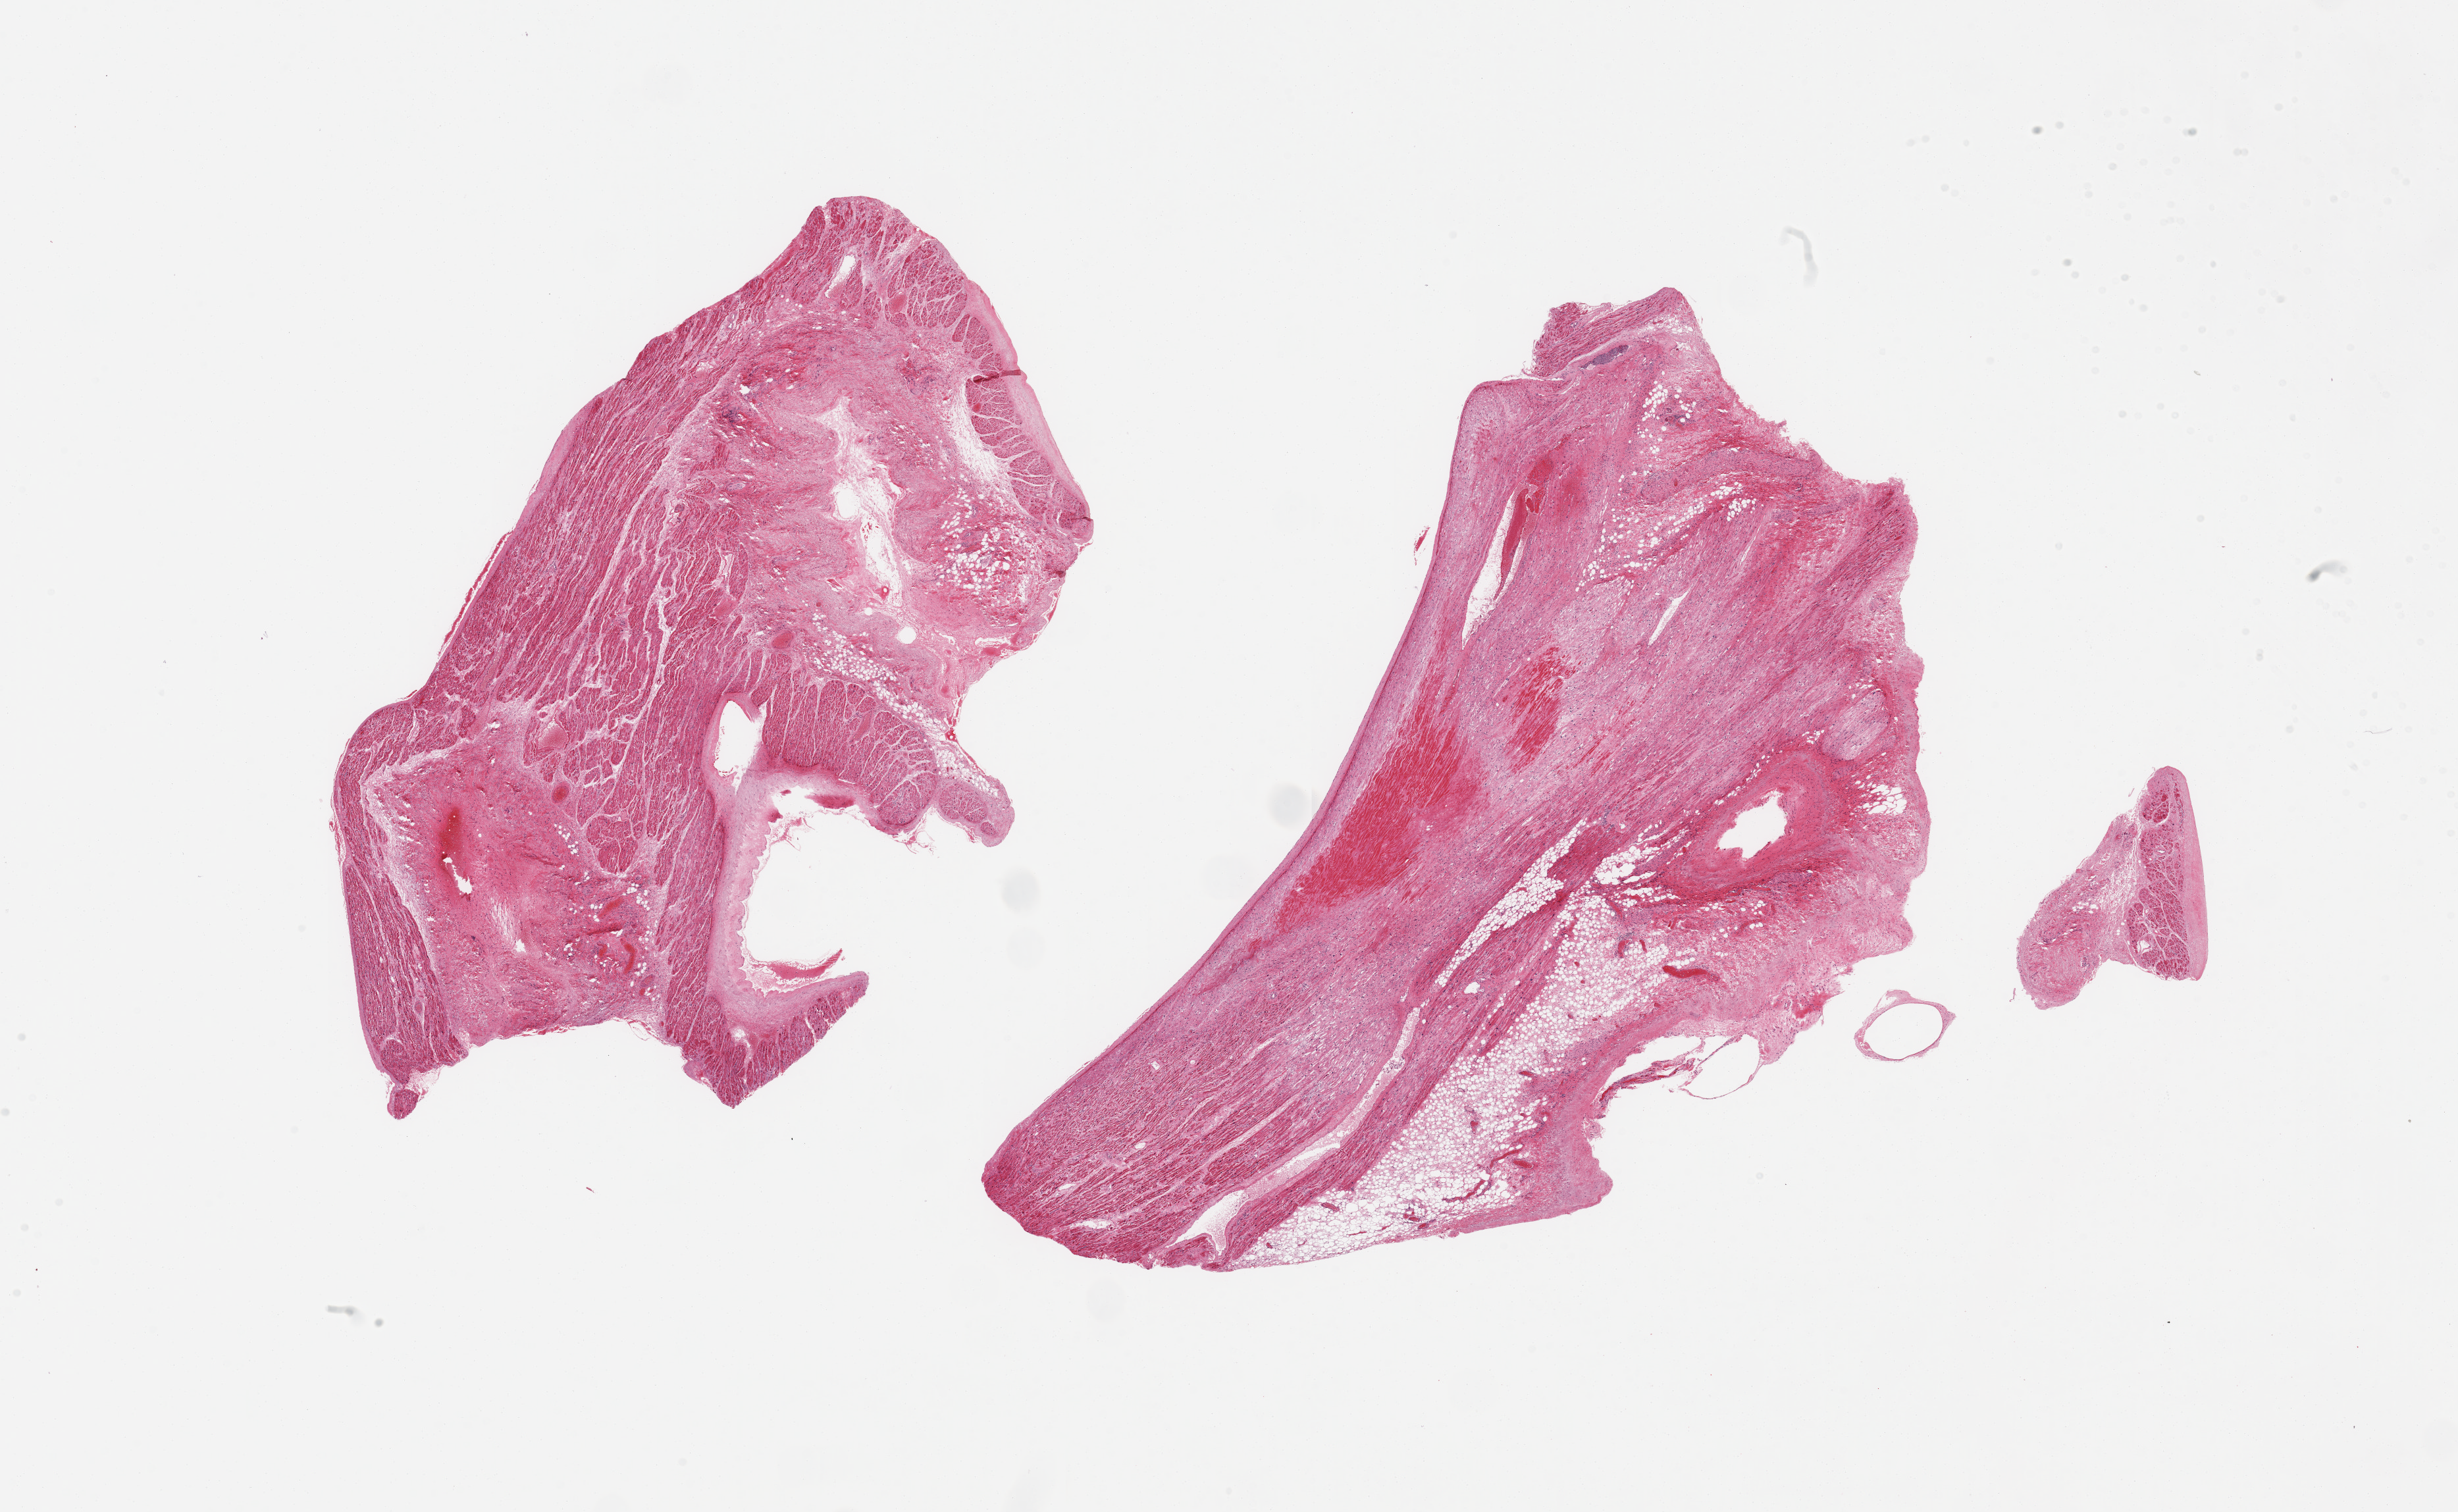
Whole-slide image, H&E stain — low-resolution overview of the scanned area, about 29.5 x 18.2 mm (acquisition: 20x scan). PAXgene-fixed paraffin-embedded (PFPE) section. Target tissue: auricular appendage. Donor tissue sample. Donor: male.
Pathologist's review note for this sample: 2 pieces; 40% fibrofatty content in 1 piece.